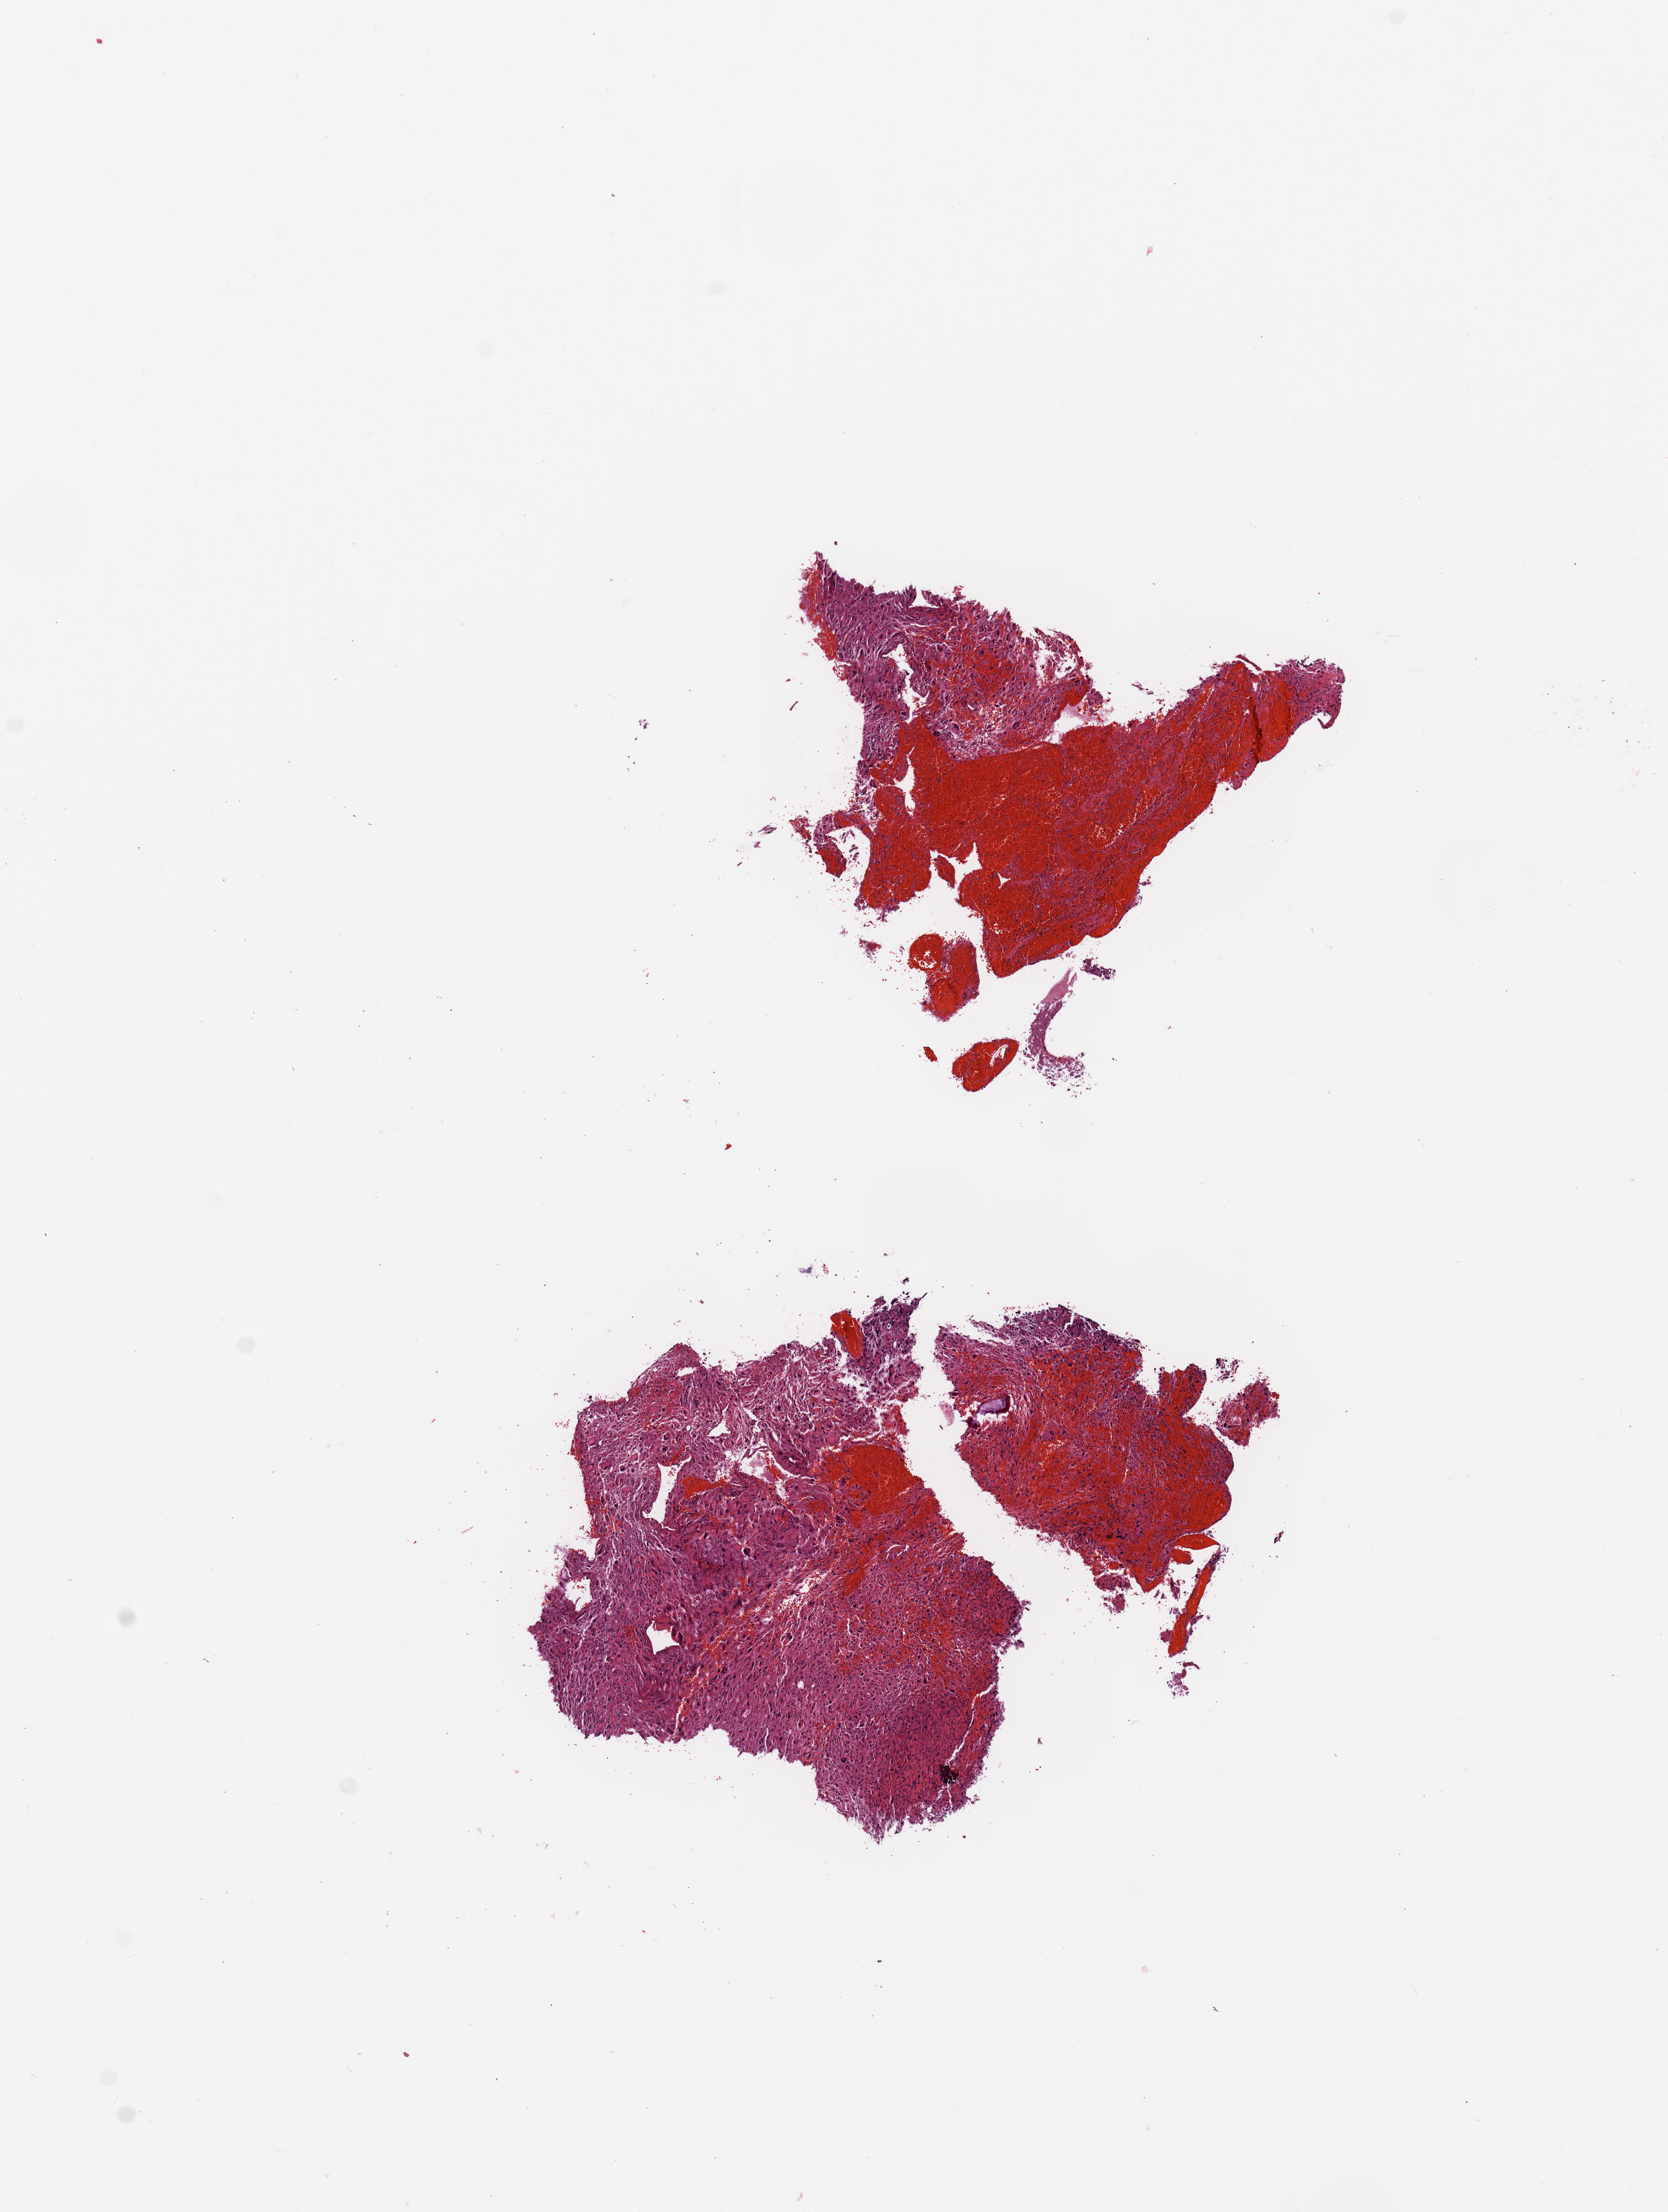
H&E-stained whole-slide image — low-resolution overview of the scanned area, about 8.9 x 11.8 mm (from a 20x scan). Tumour tissue sample, sampled site: frontal lobe. 69-year-old female patient. Pathologist review of this section (percent, as recorded): tumour nuclei 80%, necrosis 5%.
Primary tumour site (as recorded): frontal lobe. Histologic diagnosis: Glioblastoma.